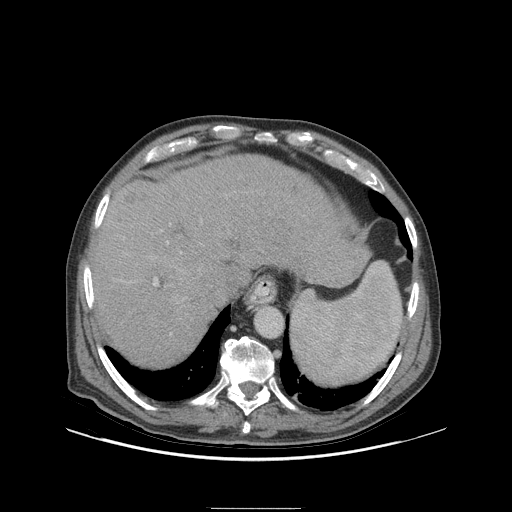
Contrast-enhanced abdominal CT (liver protocol), one axial slice; reconstruction kernel STANDARD; 140 kVp; soft-tissue window (W 400 / L 40 HU); 2.5 mm slice thickness; 512 × 512 image matrix, field of view 440 × 440 mm. From the clinical record (not read from this slice): diagnosis: hepatocellular carcinoma (patient treated with transarterial chemoembolisation; whether this scan precedes or follows treatment is not stated here); TNM stage (as recorded): Stage-I; Child-Pugh class: A; tumour nodularity: uninodular; tumour size: 5.1 cm.
Outlined on this slice (semi-automatic segmentation, software-assisted and operator-edited):
- abdominal aorta: bounding box (x1, y1, x2, y2) in pixels: (255, 307, 283, 337)
- liver parenchyma outside the tumour (the mass and vessels are separate outlines, so this box may not span the whole liver): (92, 154, 361, 366)
- liver vessels: (130, 230, 168, 286)